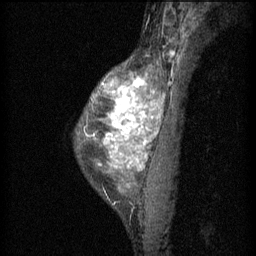
Breast MRI (dynamic contrast-enhanced), one sagittal slice; position 42 of 60 along the scan axis; 3 images stored at this slice position (order not interpretable as contrast timing); 1.5 T; TE 4.2 ms, TR 11 ms; 2 mm slice thickness; 256 × 256 image matrix, field of view 180 × 180 mm. Female patient, age 40 years.
Structures marked on this image (semi-automatically segmented with operator editing):
- analysis volume of interest (the breast-tissue region the enhancement analysis was run in; not a lesion): bounding box (x1, y1, x2, y2) in pixels: (78, 54, 172, 201)
- tumour enhancement mask (voxels above the 70 % enhancement threshold inside the analysis volume of interest): (87, 78, 163, 169)